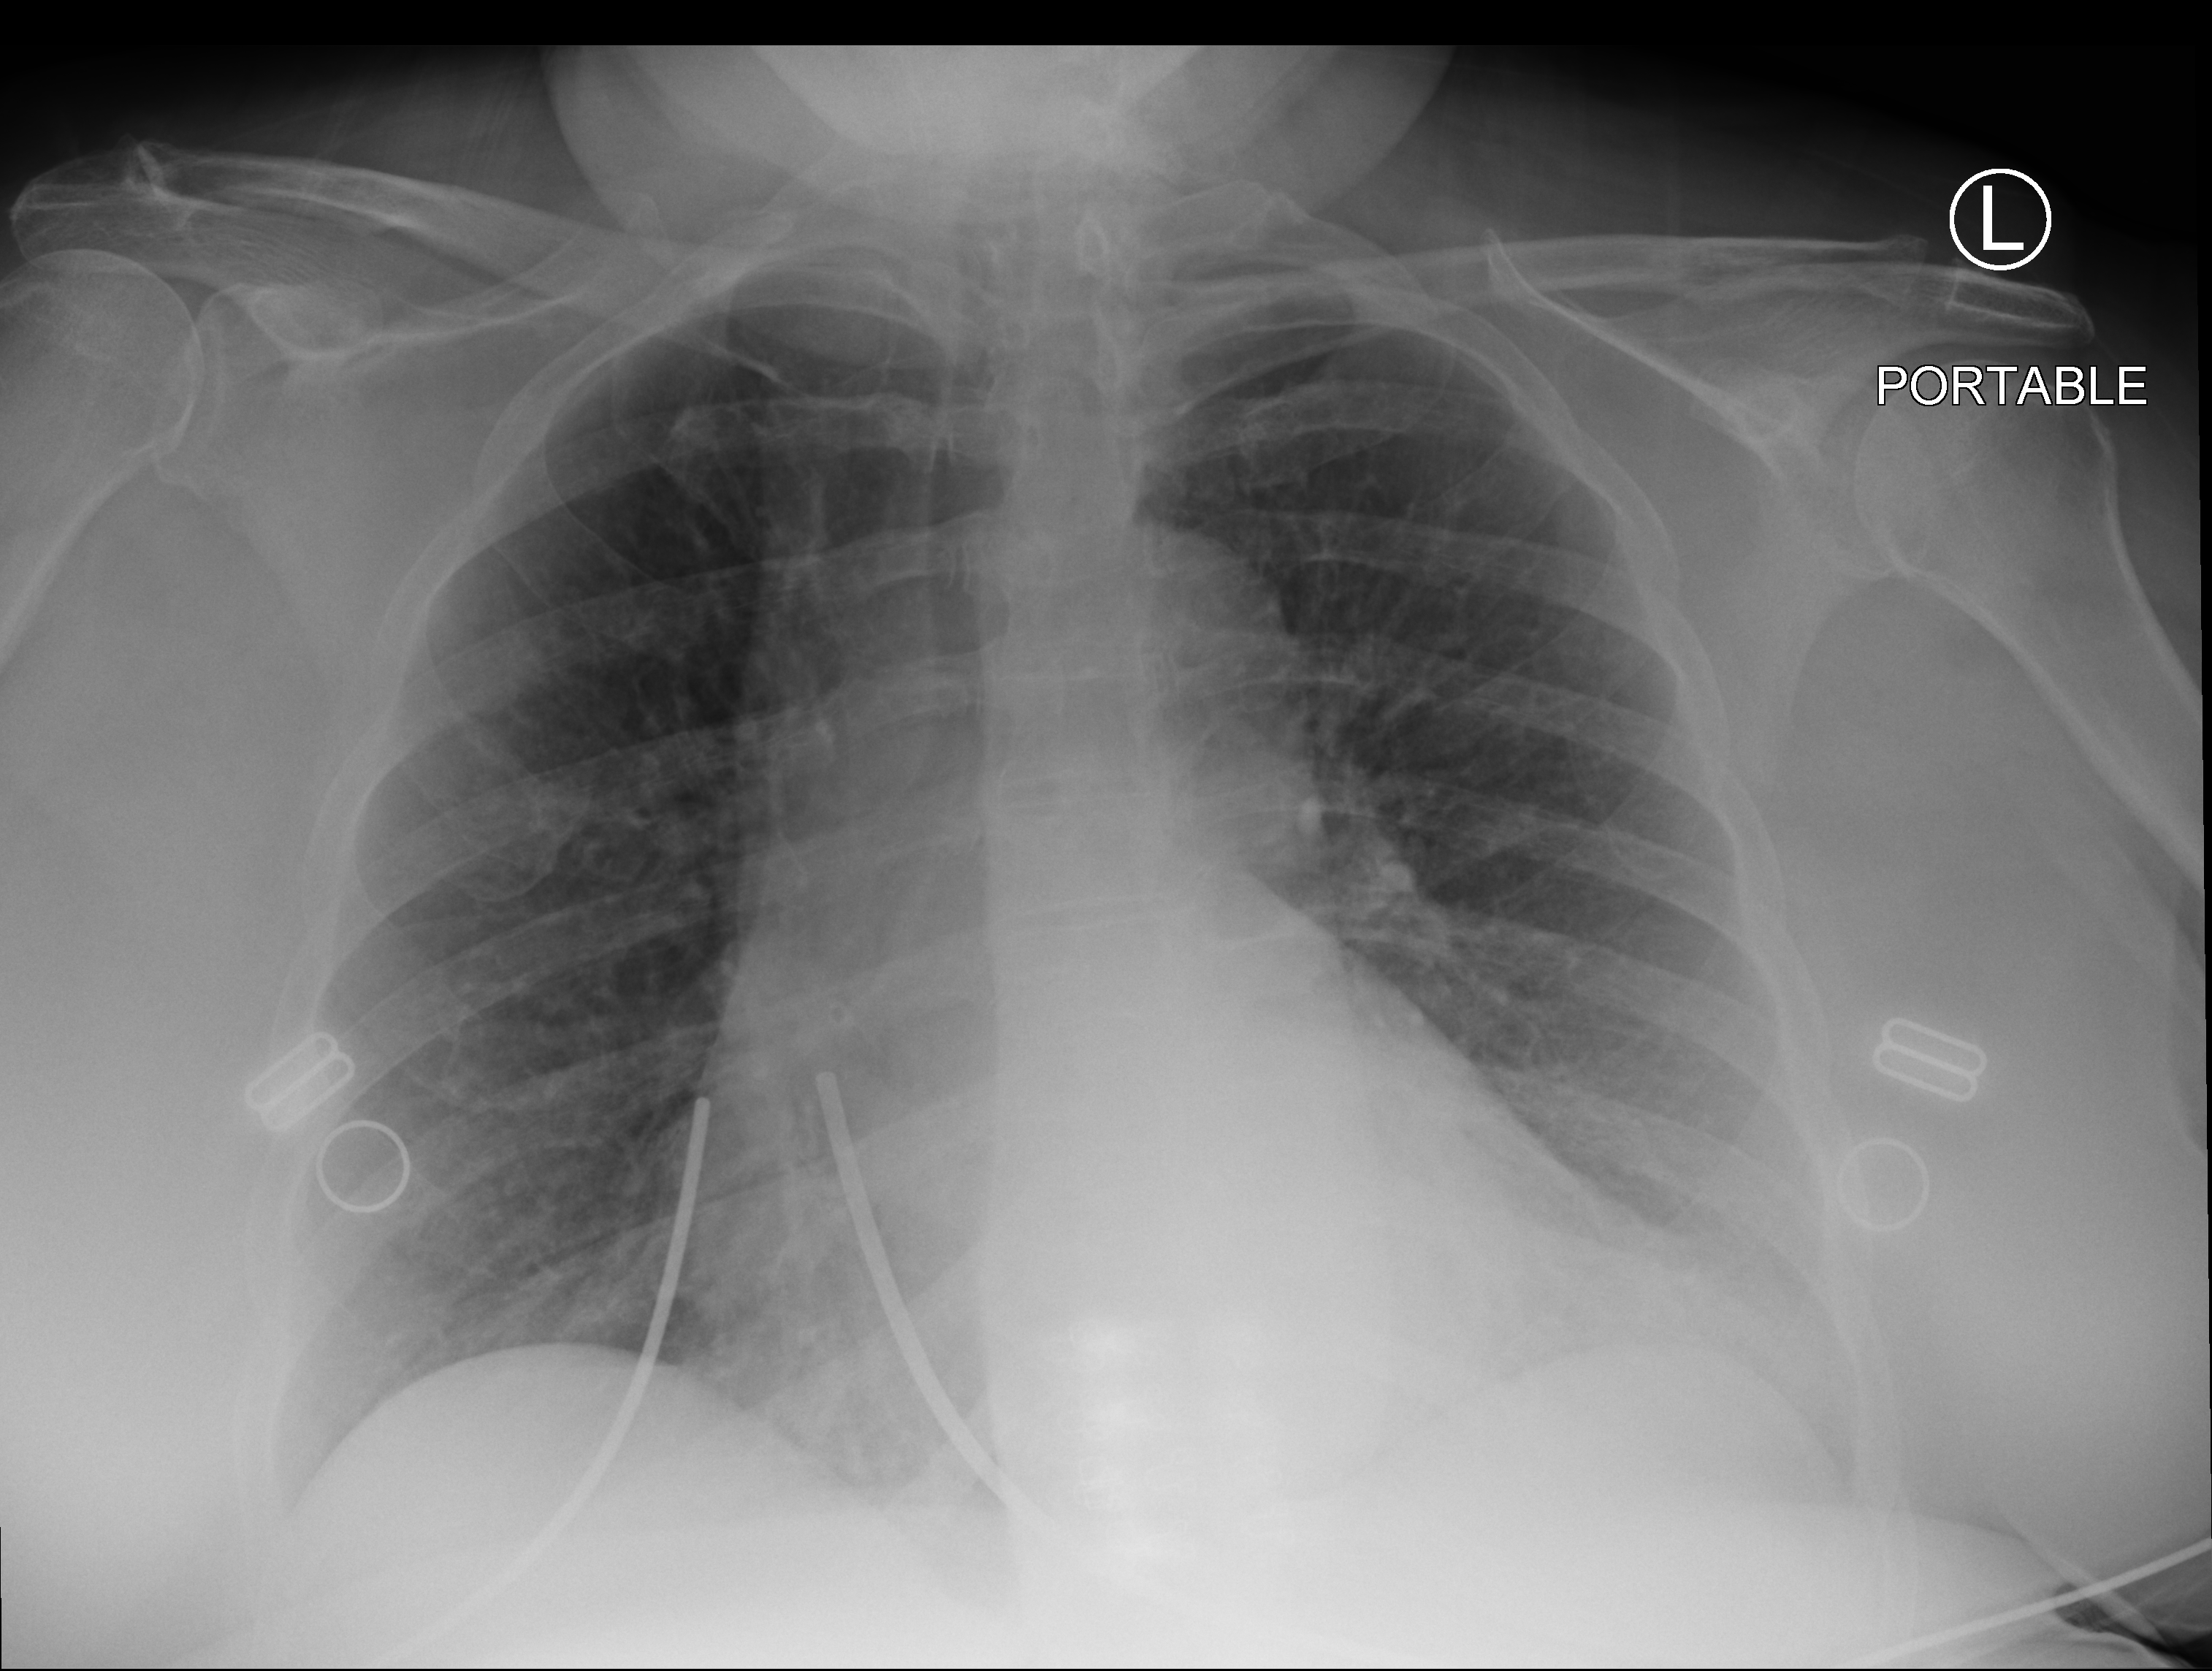
Bedside chest radiograph (computed radiography), anteroposterior (AP) projection. Female patient hospitalised with COVID-19, age 60–74 years.
Admission-level facts for this patient (not findings on this image; timing relative to this image not recorded):
- mechanically ventilated during this hospital stay: no
- other chronic lung disease (admission record): no
- admitted to intensive care during this hospital stay: no